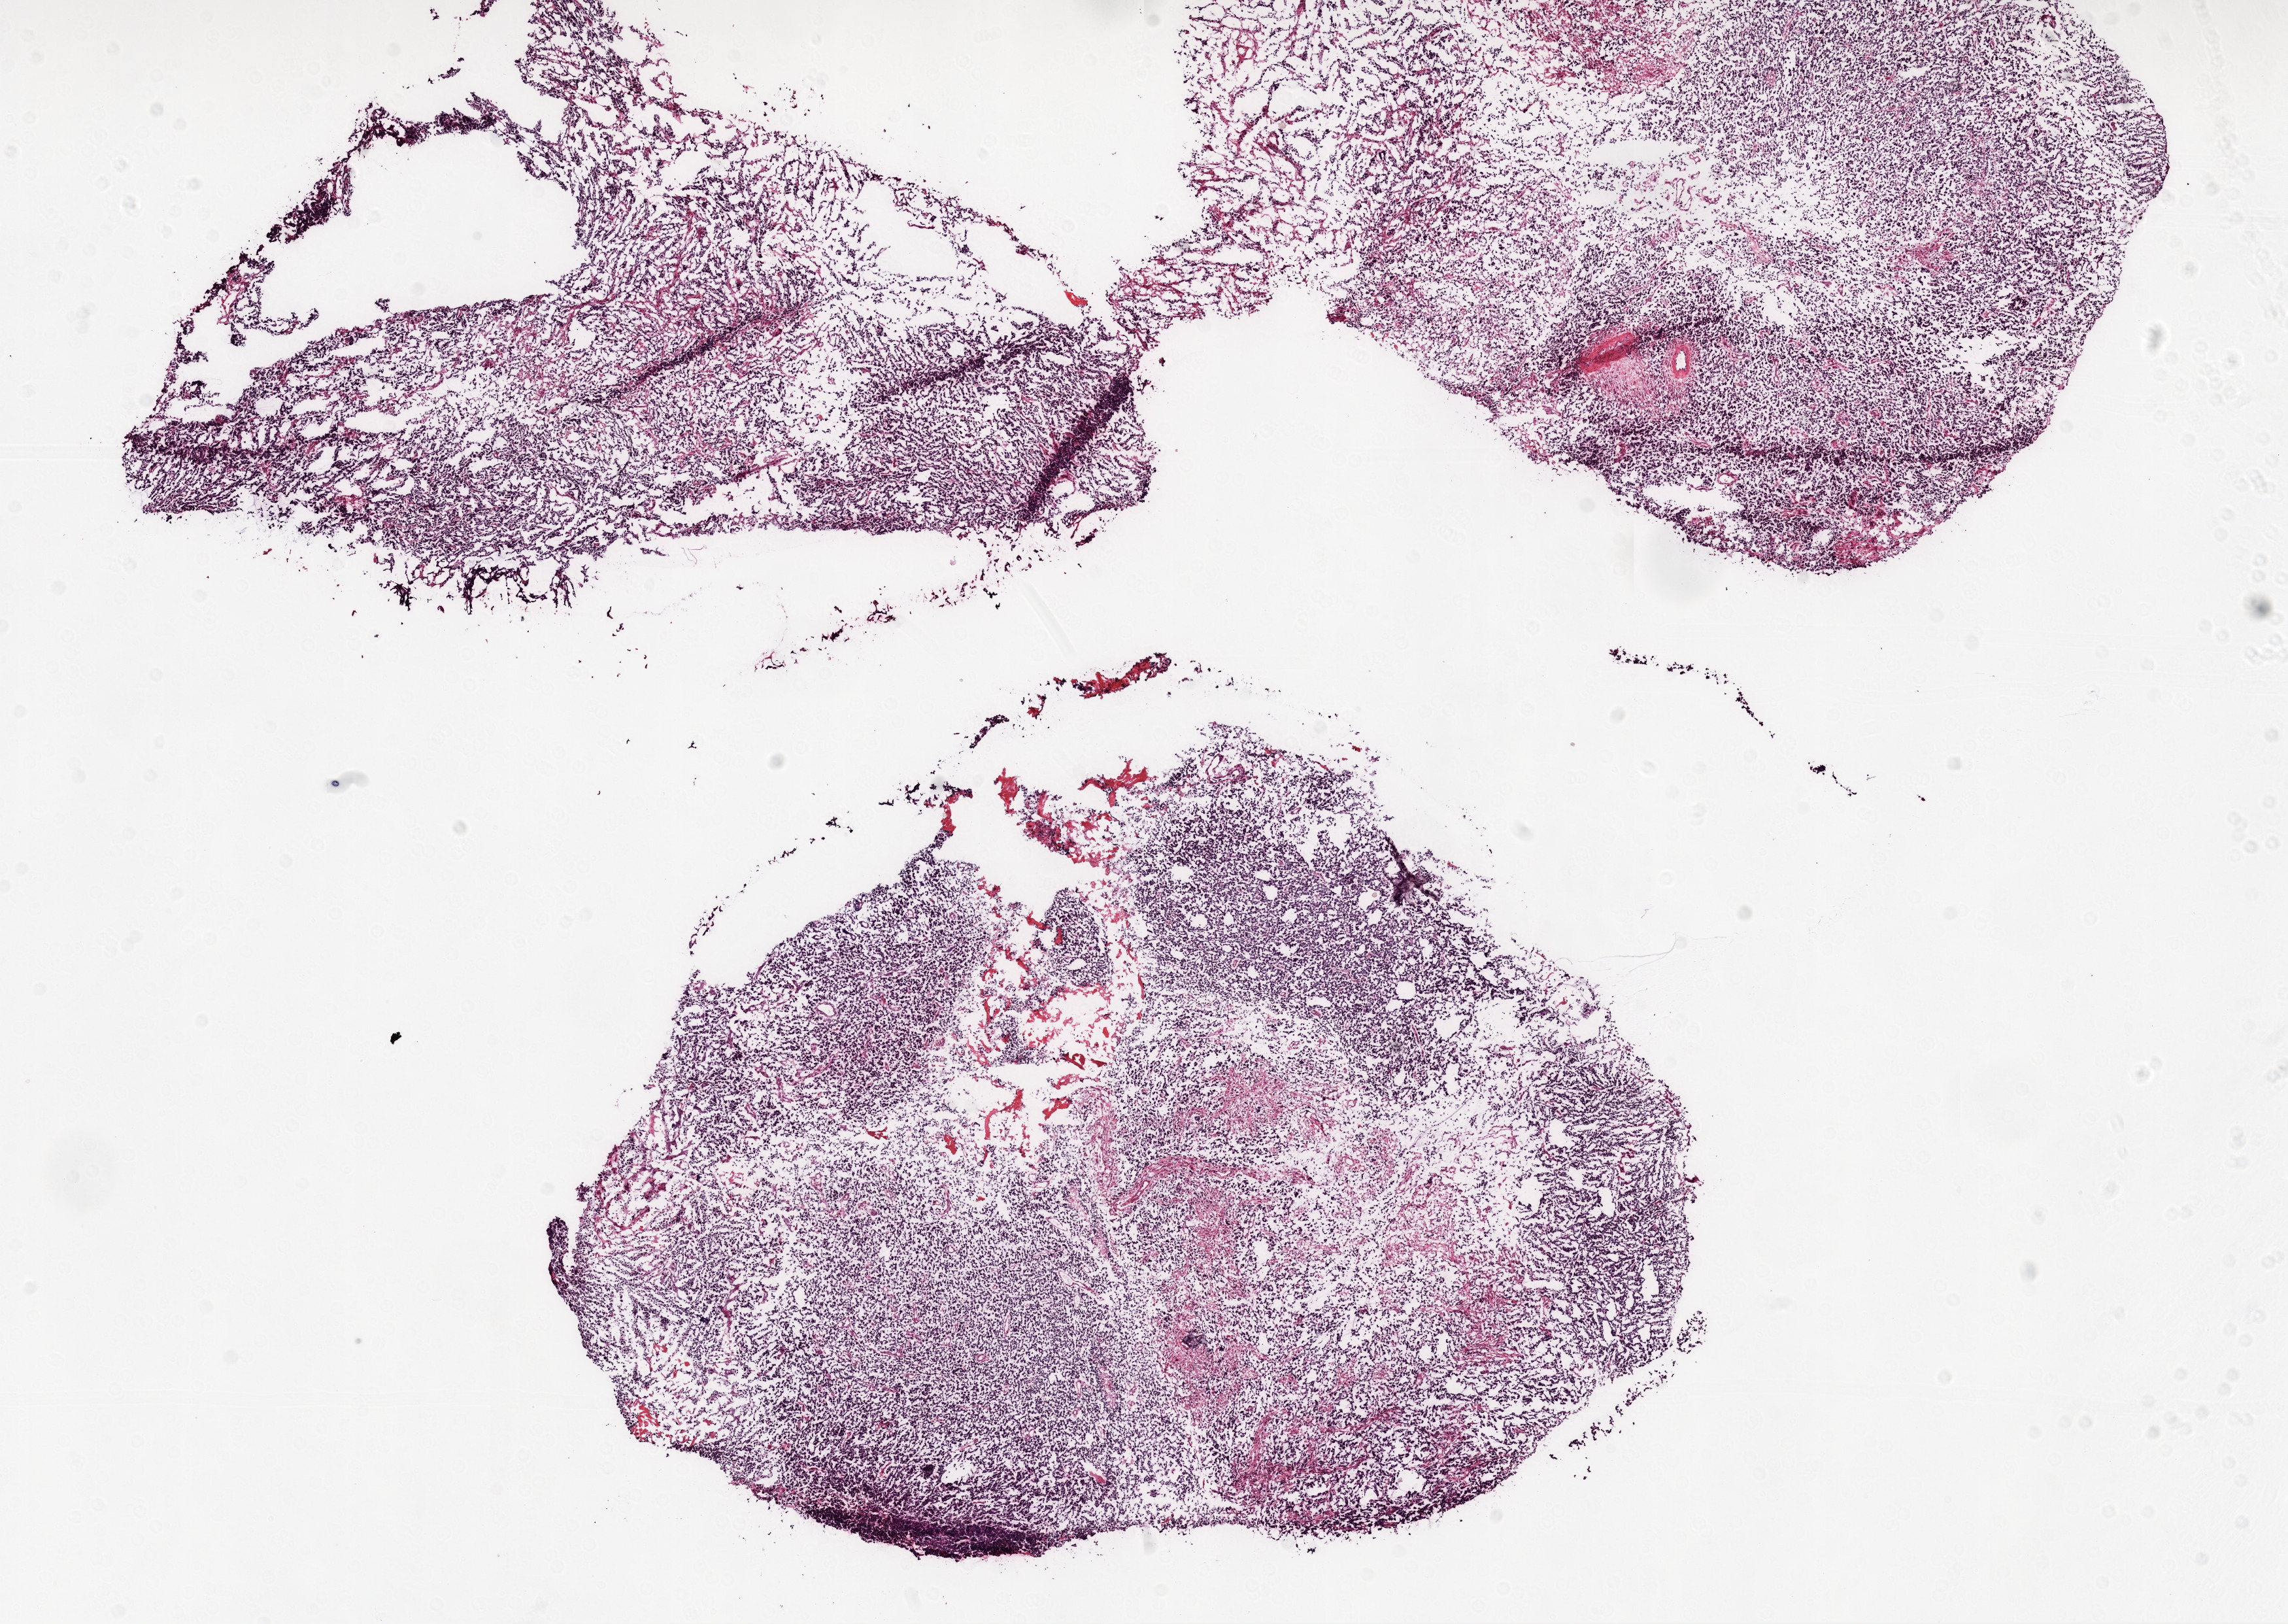
Digitized Hematoxylin and eosin (H&E) stained tissue section (whole slide) — a low-resolution overview of the entire scanned area, about 14.0 x 10.0 mm (slide scanned at 20x). Frozen section. Brain, primary tumour sample. Patient: male, age at initial diagnosis 31 years. Composition of this section per pathologist review: tumour cells 90%, tumour nuclei 95%, normal cells 0%, stromal cells 5%, necrosis 5%. Infiltration values recorded for this section: lymphocyte infiltration 100%, monocyte infiltration 0%, neutrophil infiltration 0%.
- diagnosis: Glioblastoma